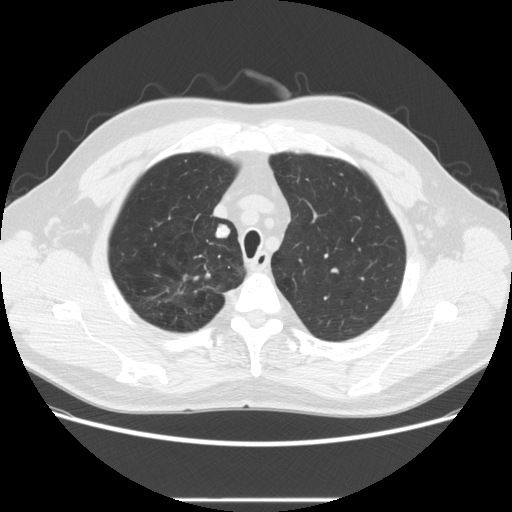
Axial slice from a low-dose chest CT screening exam; baseline annual screen; lung window (W 1500 / L -600 HU); 120 kVp; slice 46 of 270 in the series; 512 × 512 image matrix. Male, age 64 years at enrolment. Former smoker at enrolment.
- Expert reader's lesion annotation, box from (x=200, y=220) to (x=237, y=250) px.
- The screening reader recorded 2 non-calcified nodules or masses ≥4 mm on this exam (right upper lobe, right upper lobe); which of them this box marks is not recorded.
- Later outcome: lung cancer diagnosed 753 days after this screen (after the third annual screen) — adenocarcinoma, NOS, right upper lobe, moderately differentiated (G2), stage IA (AJCC 6th edition), 14 mm at pathology.